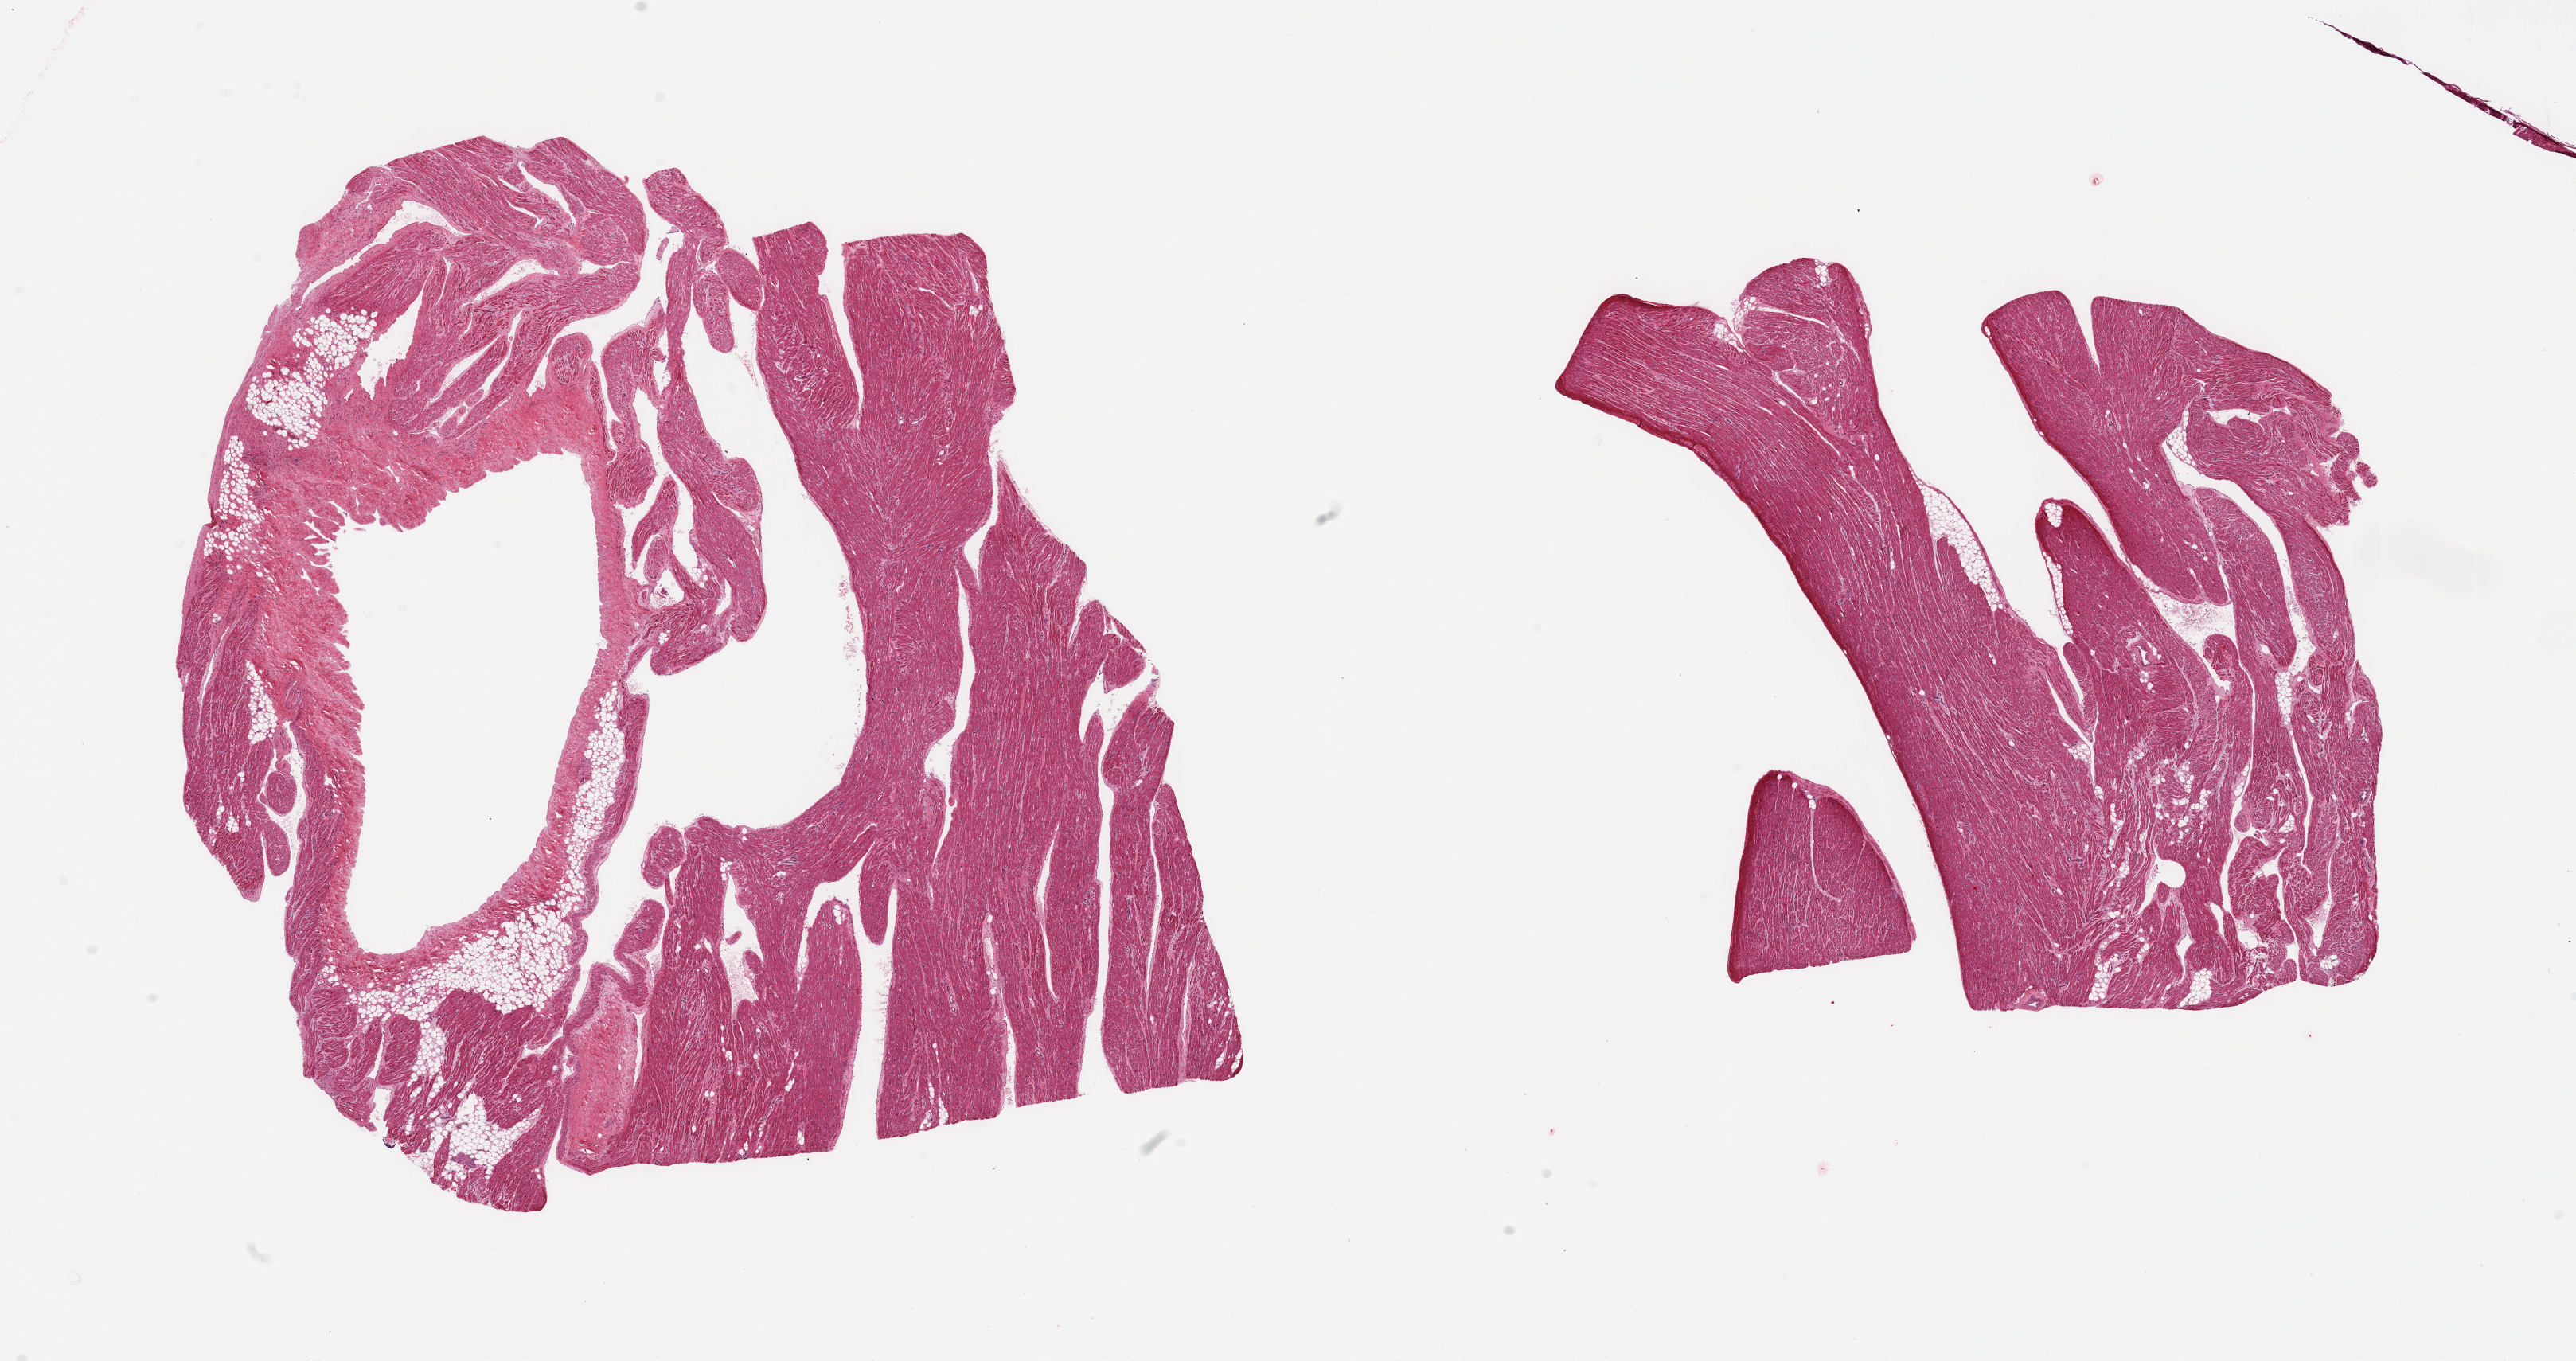
Whole-slide image, hematoxylin and eosin (H&E) stain, brightfield — whole scanned area (about 25.6 x 13.5 mm) shown as a low-resolution overview. PAXgene-fixed paraffin-embedded (PFPE) section. Section of auricular appendage (target tissue). Tissue donor sample.
- pathologist's review note for this sample: 2 pieces; 10% fat content in 1 piece